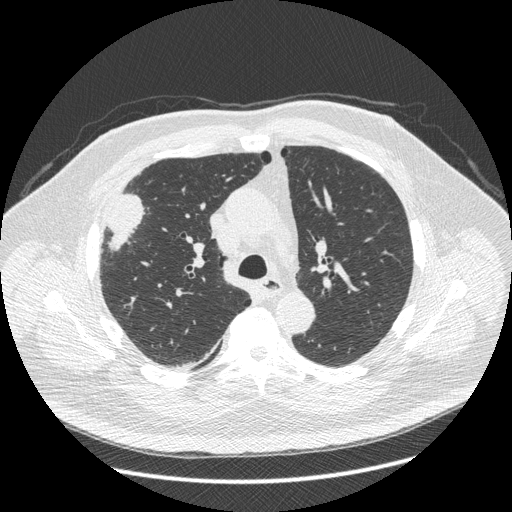
Low-dose screening chest CT, one axial slice. Slice 288 of 426 in the series (ordered by position). Reconstruction kernel STANDARD. 120 kVp. Lung window (W 1500 / L -600 HU). 1.25 mm slice thickness. 512 × 512 image matrix, field of view 400 × 400 mm.
Annotated regions visible in this slice (manually delineated by an expert):
- lesion 1 (tumor, upper lobe of right lung): bounding box [x1, y1, x2, y2] px = [106, 194, 144, 250]